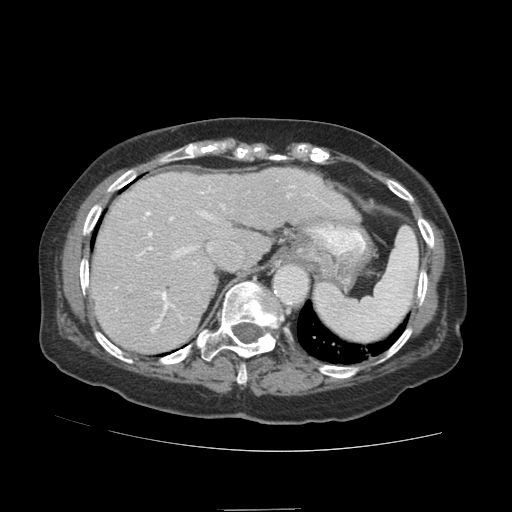
Contrast-enhanced abdominal CT (liver protocol), one axial slice; position 69 of 89 along the scan axis; reconstruction kernel STANDARD; soft-tissue window (W 400 / L 40 HU); 512 × 512 image matrix, field of view 360 × 360 mm. From the clinical record (not read from this slice): diagnosis: hepatocellular carcinoma (patient treated with transarterial chemoembolisation; whether this scan precedes or follows treatment is not stated here); TNM stage (as recorded): Stage-II; Child-Pugh class: A; tumour differentiation: moderately differentiated; tumour nodularity: multinodular.
Annotated regions visible in this slice (semi-automatically segmented with operator editing):
- liver parenchyma outside the tumour (the mass and vessels are separate outlines, so this box may not span the whole liver): box from (x=90, y=168) to (x=315, y=352) px
- liver vessels: (x=115, y=185)–(x=296, y=332)